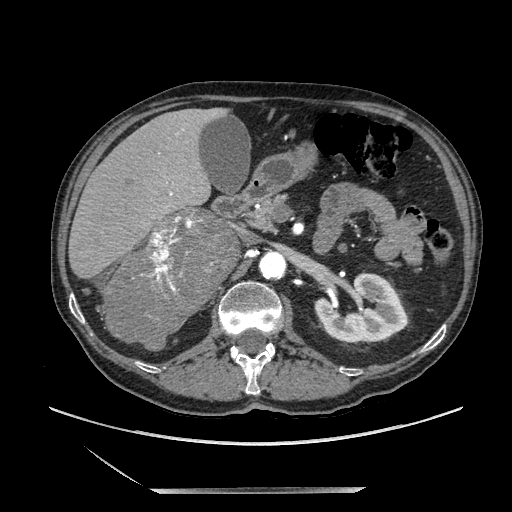
Contrast-enhanced abdominal CT, one axial slice; slice 110 of 243 in the series (ordered by position); soft-tissue window (W 400 / L 40 HU); 512 × 512 image matrix, field of view 420 × 420 mm. Male patient. From the clinical record (not read from this slice): diagnosis: adrenocortical carcinoma; tumour side: right adrenal; tumour size at pathology: 16 cm; Ki-67 index: 17 %; stage (as recorded): 3.
Outlined on this slice (semi-automatic segmentation, software-assisted and operator-edited):
- mass: bounding box (x1, y1, x2, y2) in pixels: (107, 209, 233, 345)